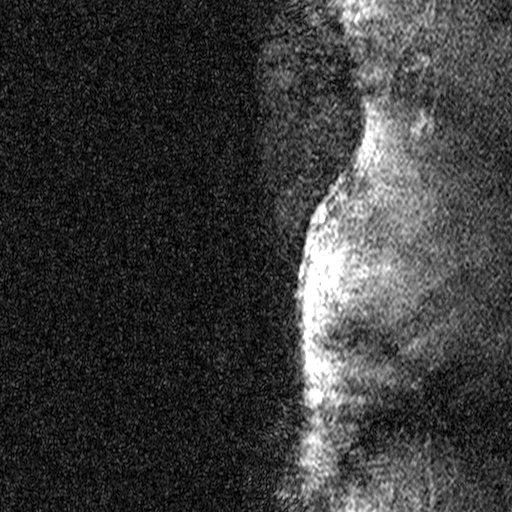
Breast MRI (dynamic contrast-enhanced), one sagittal slice; slice 40 of 44 in the series (ordered by position); dynamic contrast-enhanced study with each time point stored as its own series, time point 2 of 3 at this slice position (early post-contrast, ordered by acquisition time); 1.5 T; TE 4.5 ms, TR 11 ms; 3 mm slice thickness; 512 × 512 image matrix, field of view 200 × 200 mm. Female patient, age 44 years. From the clinical record (not read from this slice): setting: breast cancer imaged before/during neoadjuvant chemotherapy; receptor status: HR-positive, HER2-negative.
Annotated regions visible in this slice (semi-automatic segmentation, software-assisted and operator-edited):
- analysis volume of interest (the breast-tissue region the enhancement analysis was run in; not a lesion): bounding box [x1, y1, x2, y2] px = [218, 118, 341, 291]
- tumour enhancement mask (voxels above the 90 % enhancement threshold inside the analysis volume of interest): [317, 212, 327, 283]